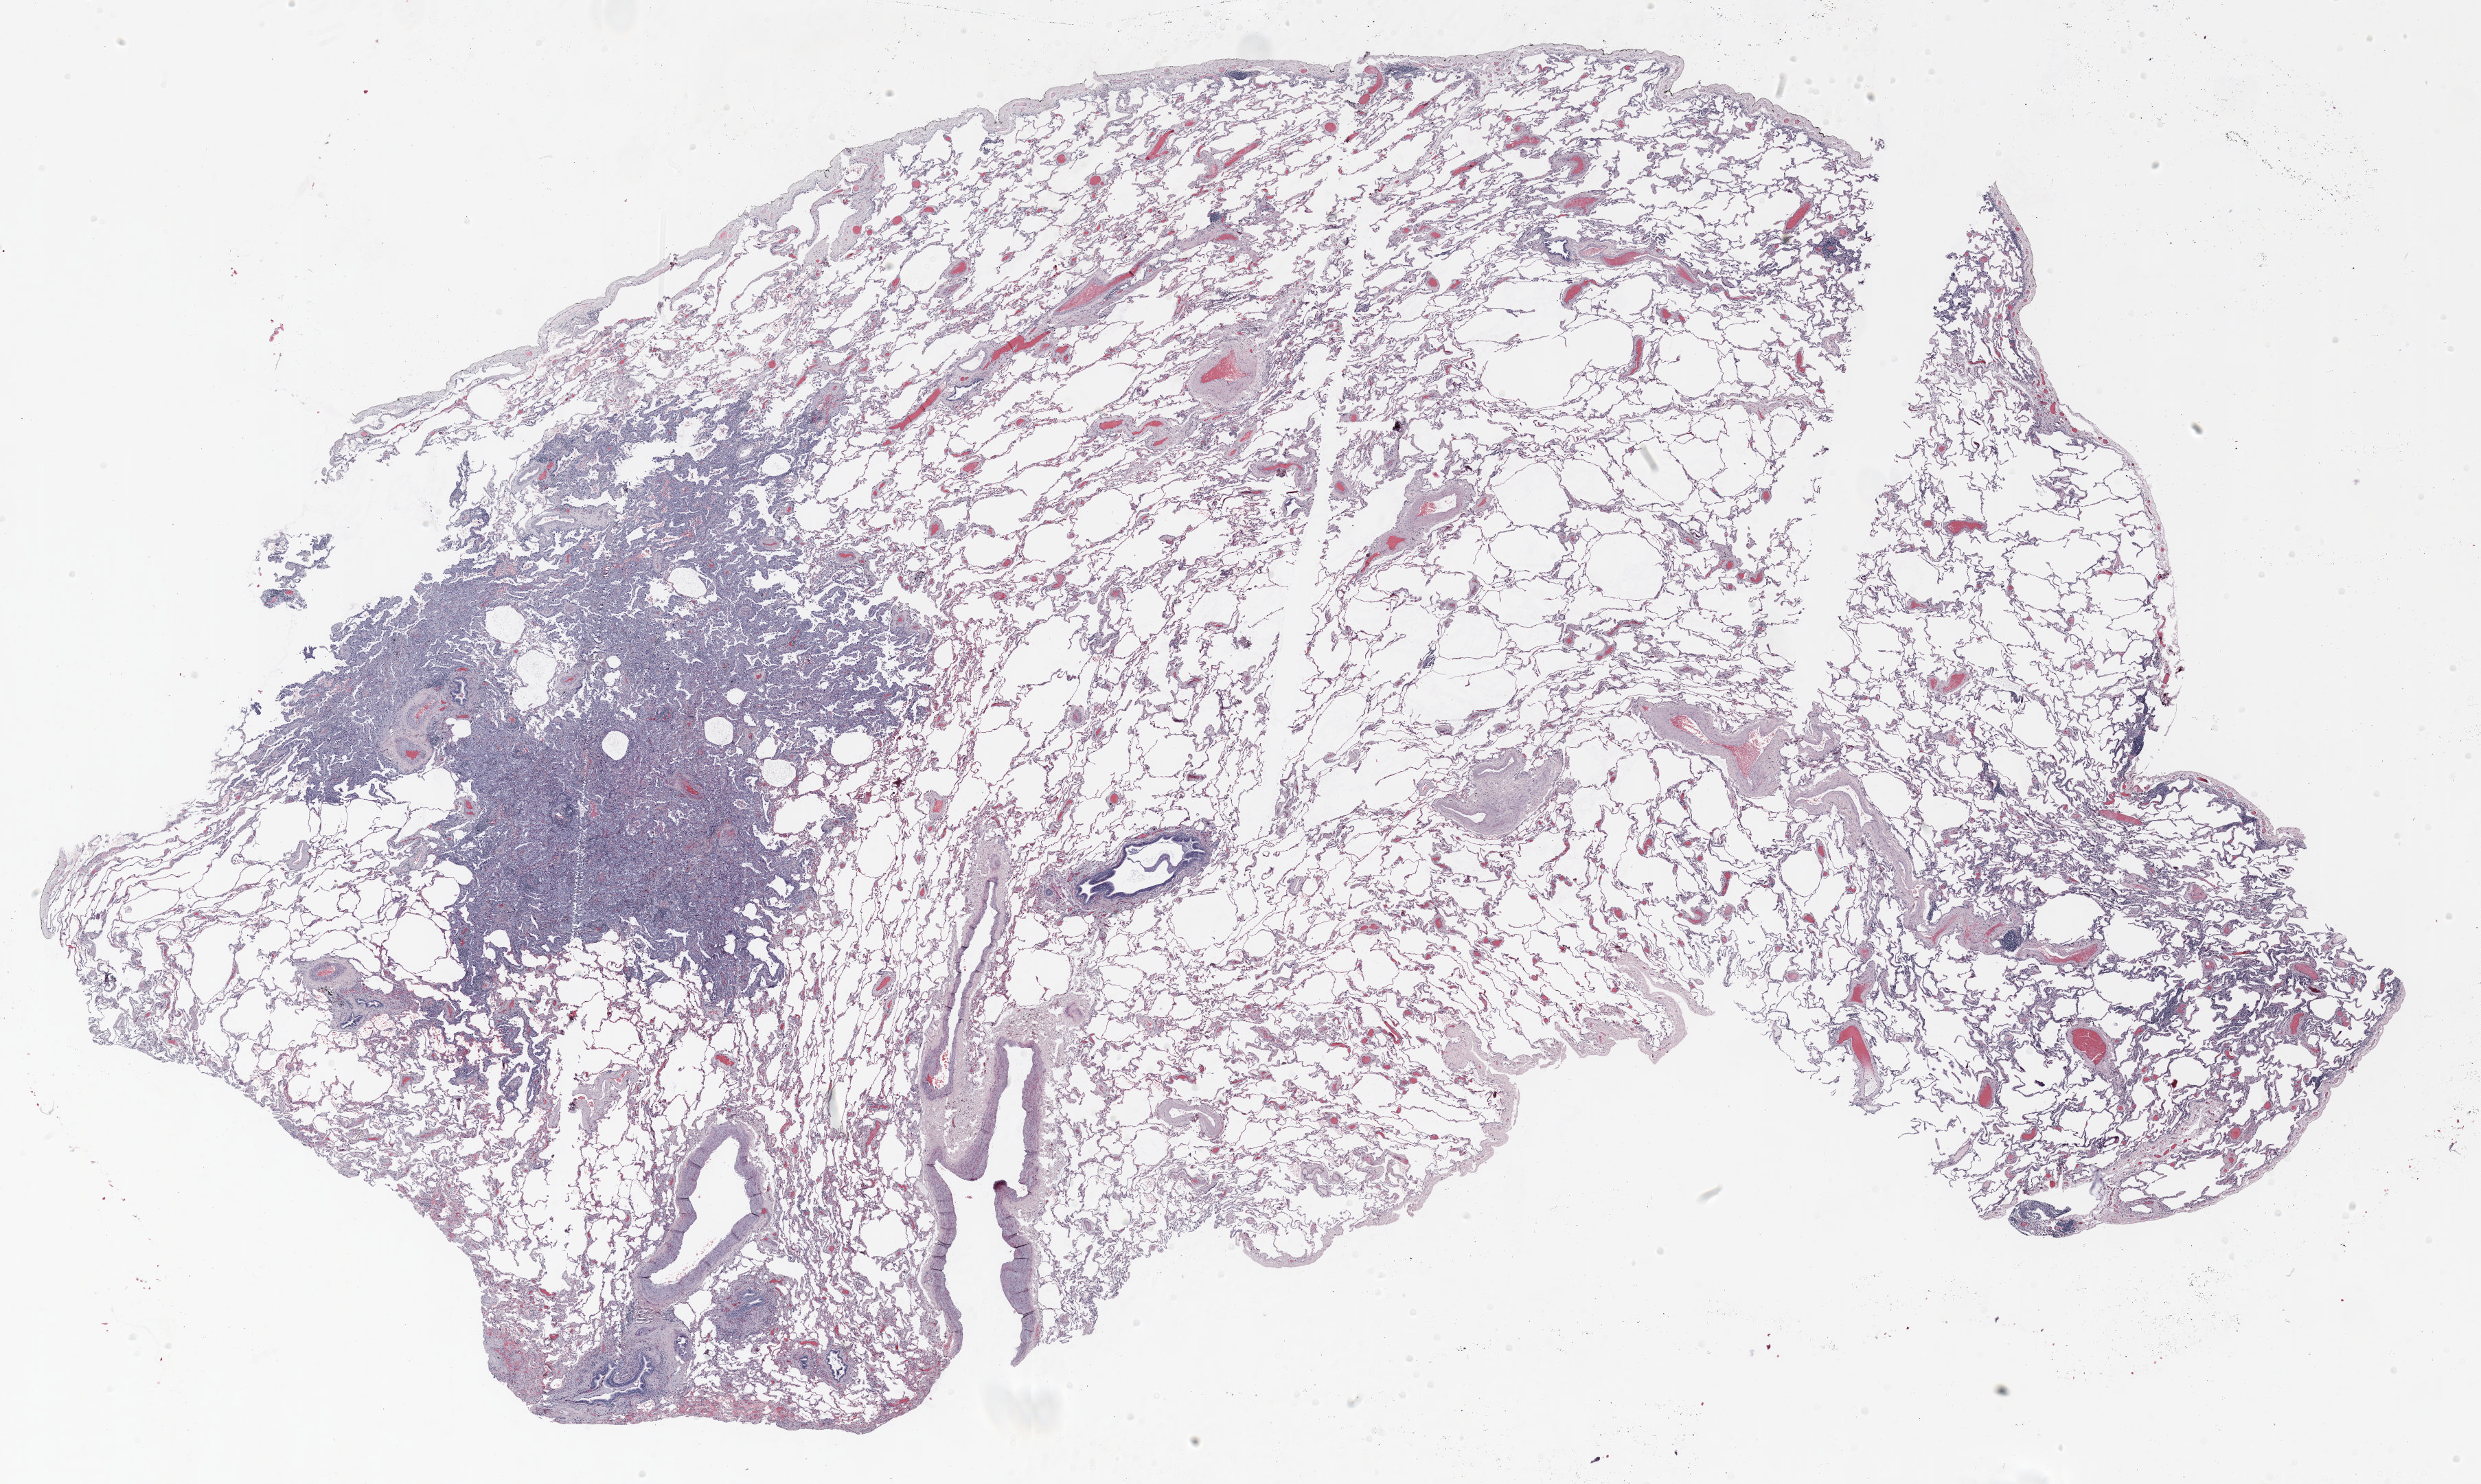
Whole-slide histology image, H&E-stained — low-resolution overview of the scanned area, about 29.0 x 17.4 mm. Formalin-fixed paraffin-embedded (FFPE) section. Lung. Female, age 66 at enrolment. Former smoker at enrolment. Grade: moderately differentiated (G2).
* tumour size (pathology): 11 mm
* stage (AJCC 6th edition): IA
* participant's lung-cancer diagnosis: Adenocarcinoma, NOS (ICD-O-3 8140/3)
* primary tumour location (clinical record): right middle lobe